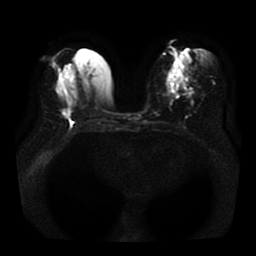
Breast MRI, one axial slice. Slice 16 of 41 in the series (ordered by position). Diffusion-weighted series; image 2 of 4 stored at this slice position (different b-values; order by instance number). 1.5 T. 5 mm slice thickness. 256 × 256 image matrix. Female patient.
Structures marked on this image (expert manual segmentation):
- tumour on diffusion-weighted imaging: bounding box (x1, y1, x2, y2) in pixels: (62, 109, 72, 118)